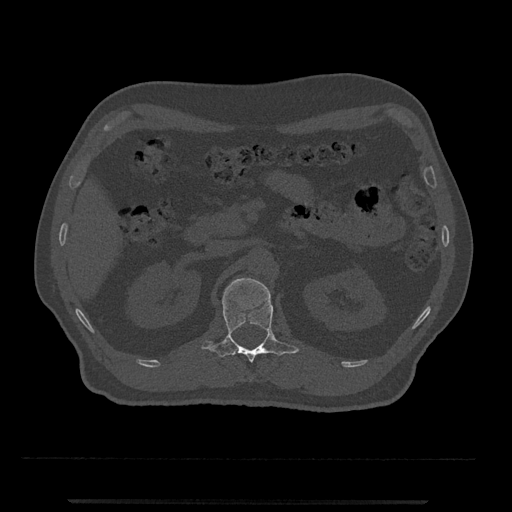
CT including the spine, one axial slice. Slice 338 of 797 in the series (ordered by position). Reconstruction kernel Br40s/3. 120 kVp. Bone window (W 1800 / L 400 HU). 512 × 512 image matrix. Male patient, age 63 years. From the clinical record (not read from this slice): primary cancer: prostate.
Outlined on this slice (semi-automatic segmentation, software-assisted and operator-edited):
- L1 vertebra: box from (x=201, y=278) to (x=299, y=381) px